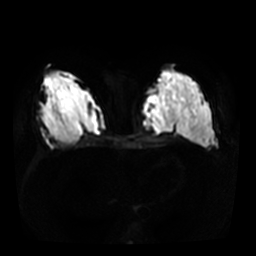
Breast MRI, one axial slice. Slice 15 of 36 in the series (ordered by position). Diffusion-weighted series; image 2 of 4 stored at this slice position (different b-values; order by instance number). 3 T. 5 mm slice thickness. 256 × 256 image matrix, field of view 340 × 340 mm. Female patient.
Outlined on this slice (outlined manually by an expert reader):
- tumour on diffusion-weighted imaging: bounding box <166,86,179,121> (left, top, right, bottom; pixels)